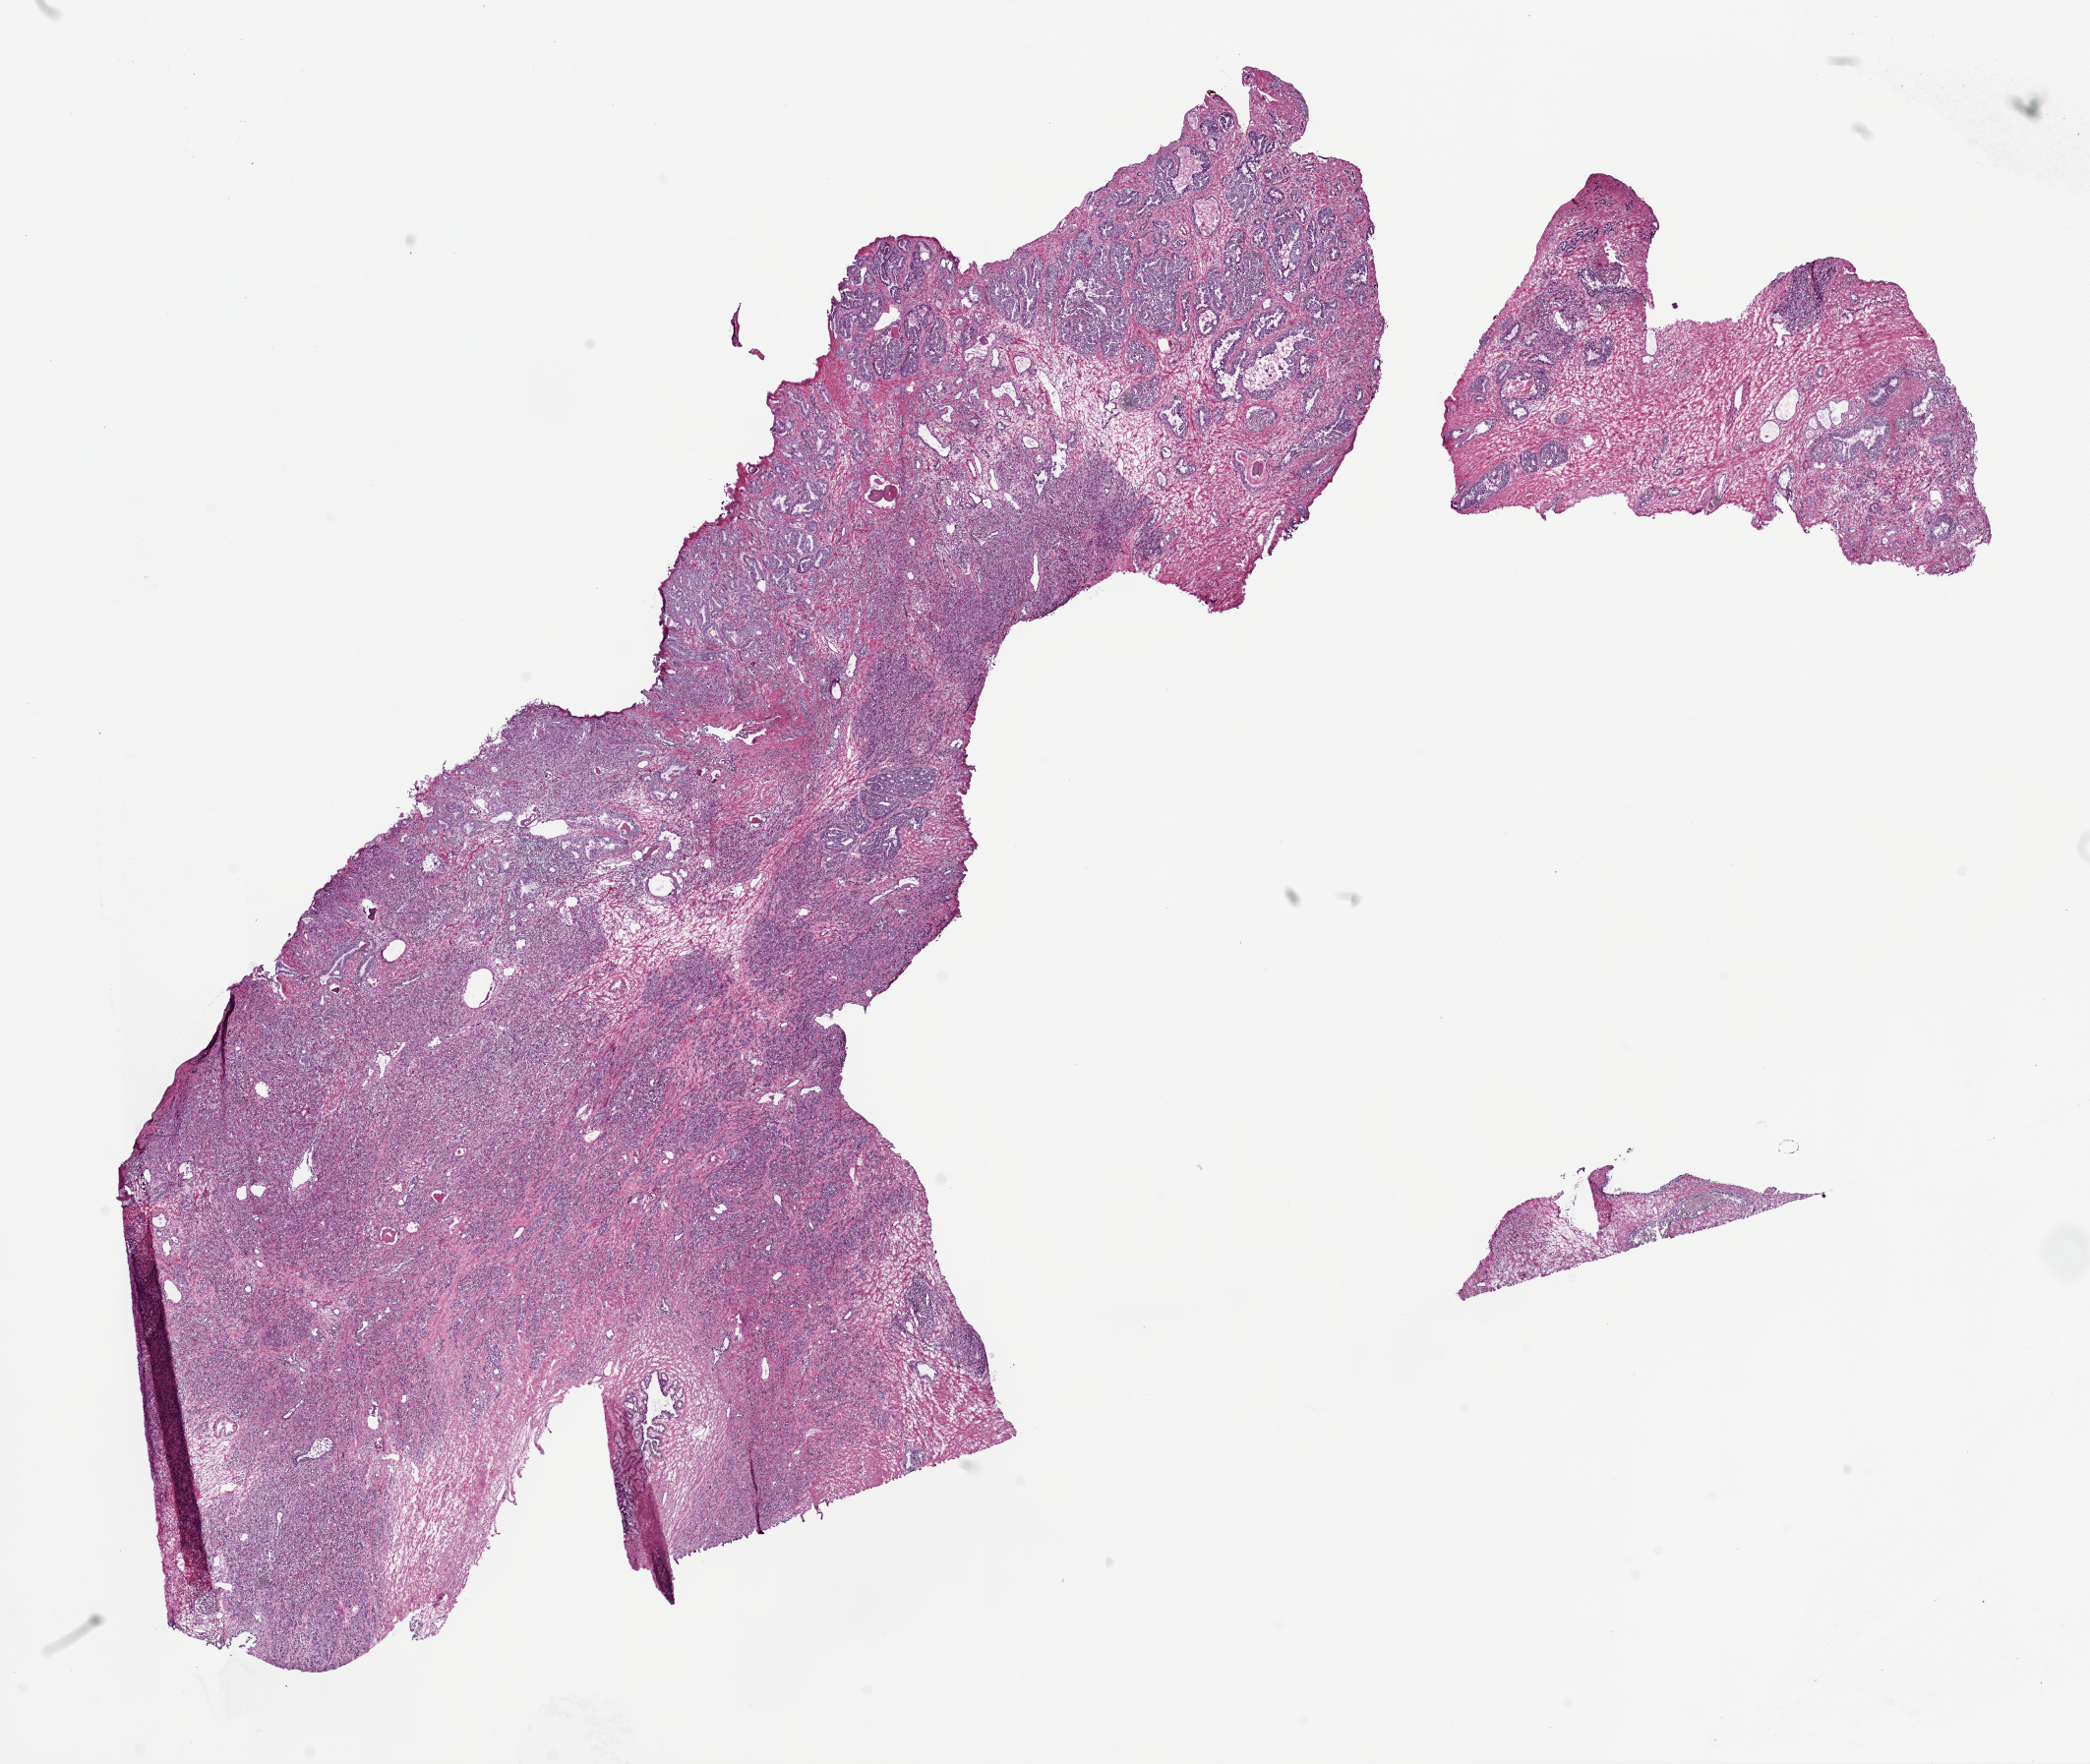
Hematoxylin and eosin (H&E) stained whole-slide image, shown as a low-resolution overview of the whole scanned area (about 17.1 x 14.4 mm); frozen section; sample: primary tumour, prostate. Patient: male, age at initial diagnosis 68 years.
Pathologic diagnosis: Acinar cell carcinoma (prostate gland).